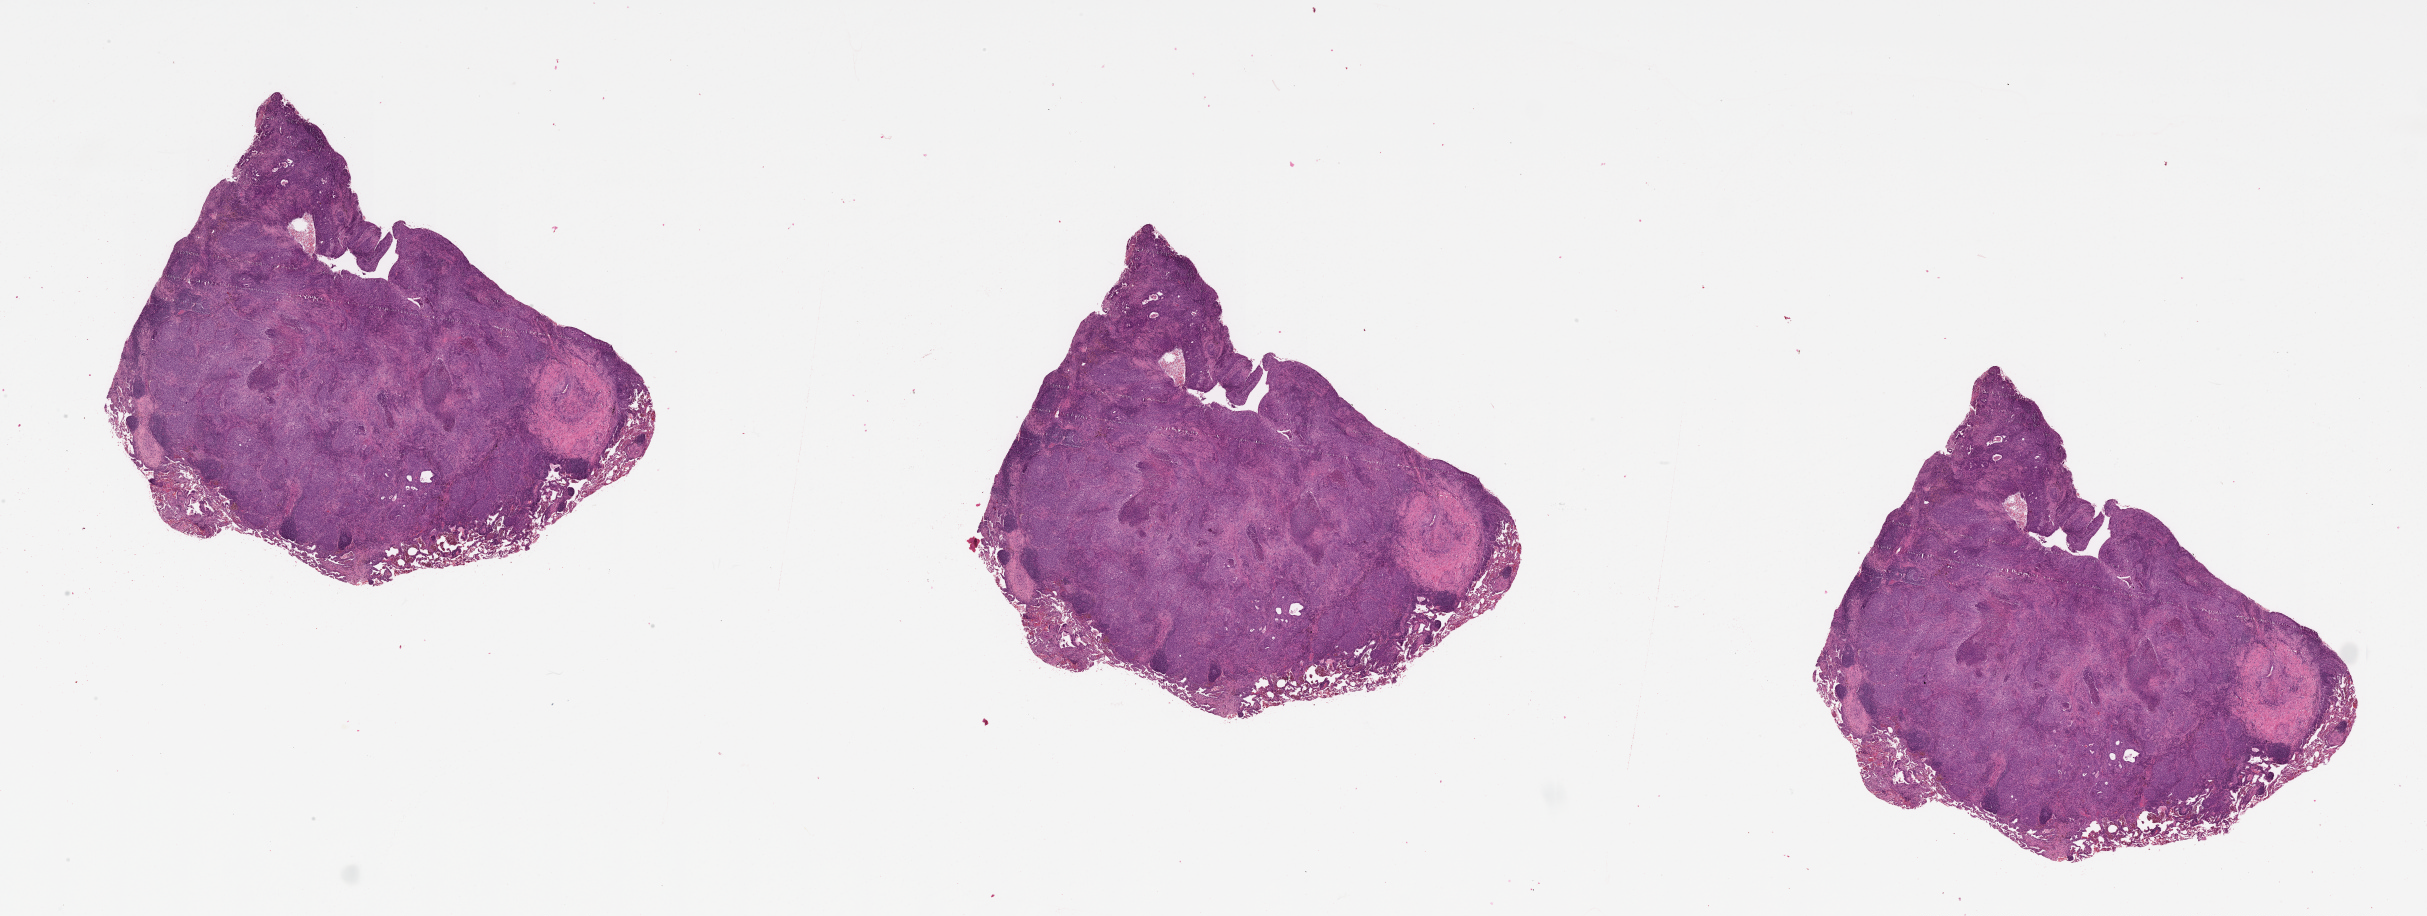
Hematoxylin and eosin (H&E) stained whole-slide image, low-resolution overview of the scanned area, about 39.1 x 14.8 mm (acquisition: 20x scan); tumour tissue sample, lung. Patient: male, age 77 years.
Patient diagnosis (cohort enrolment): squamous cell carcinoma (lung).